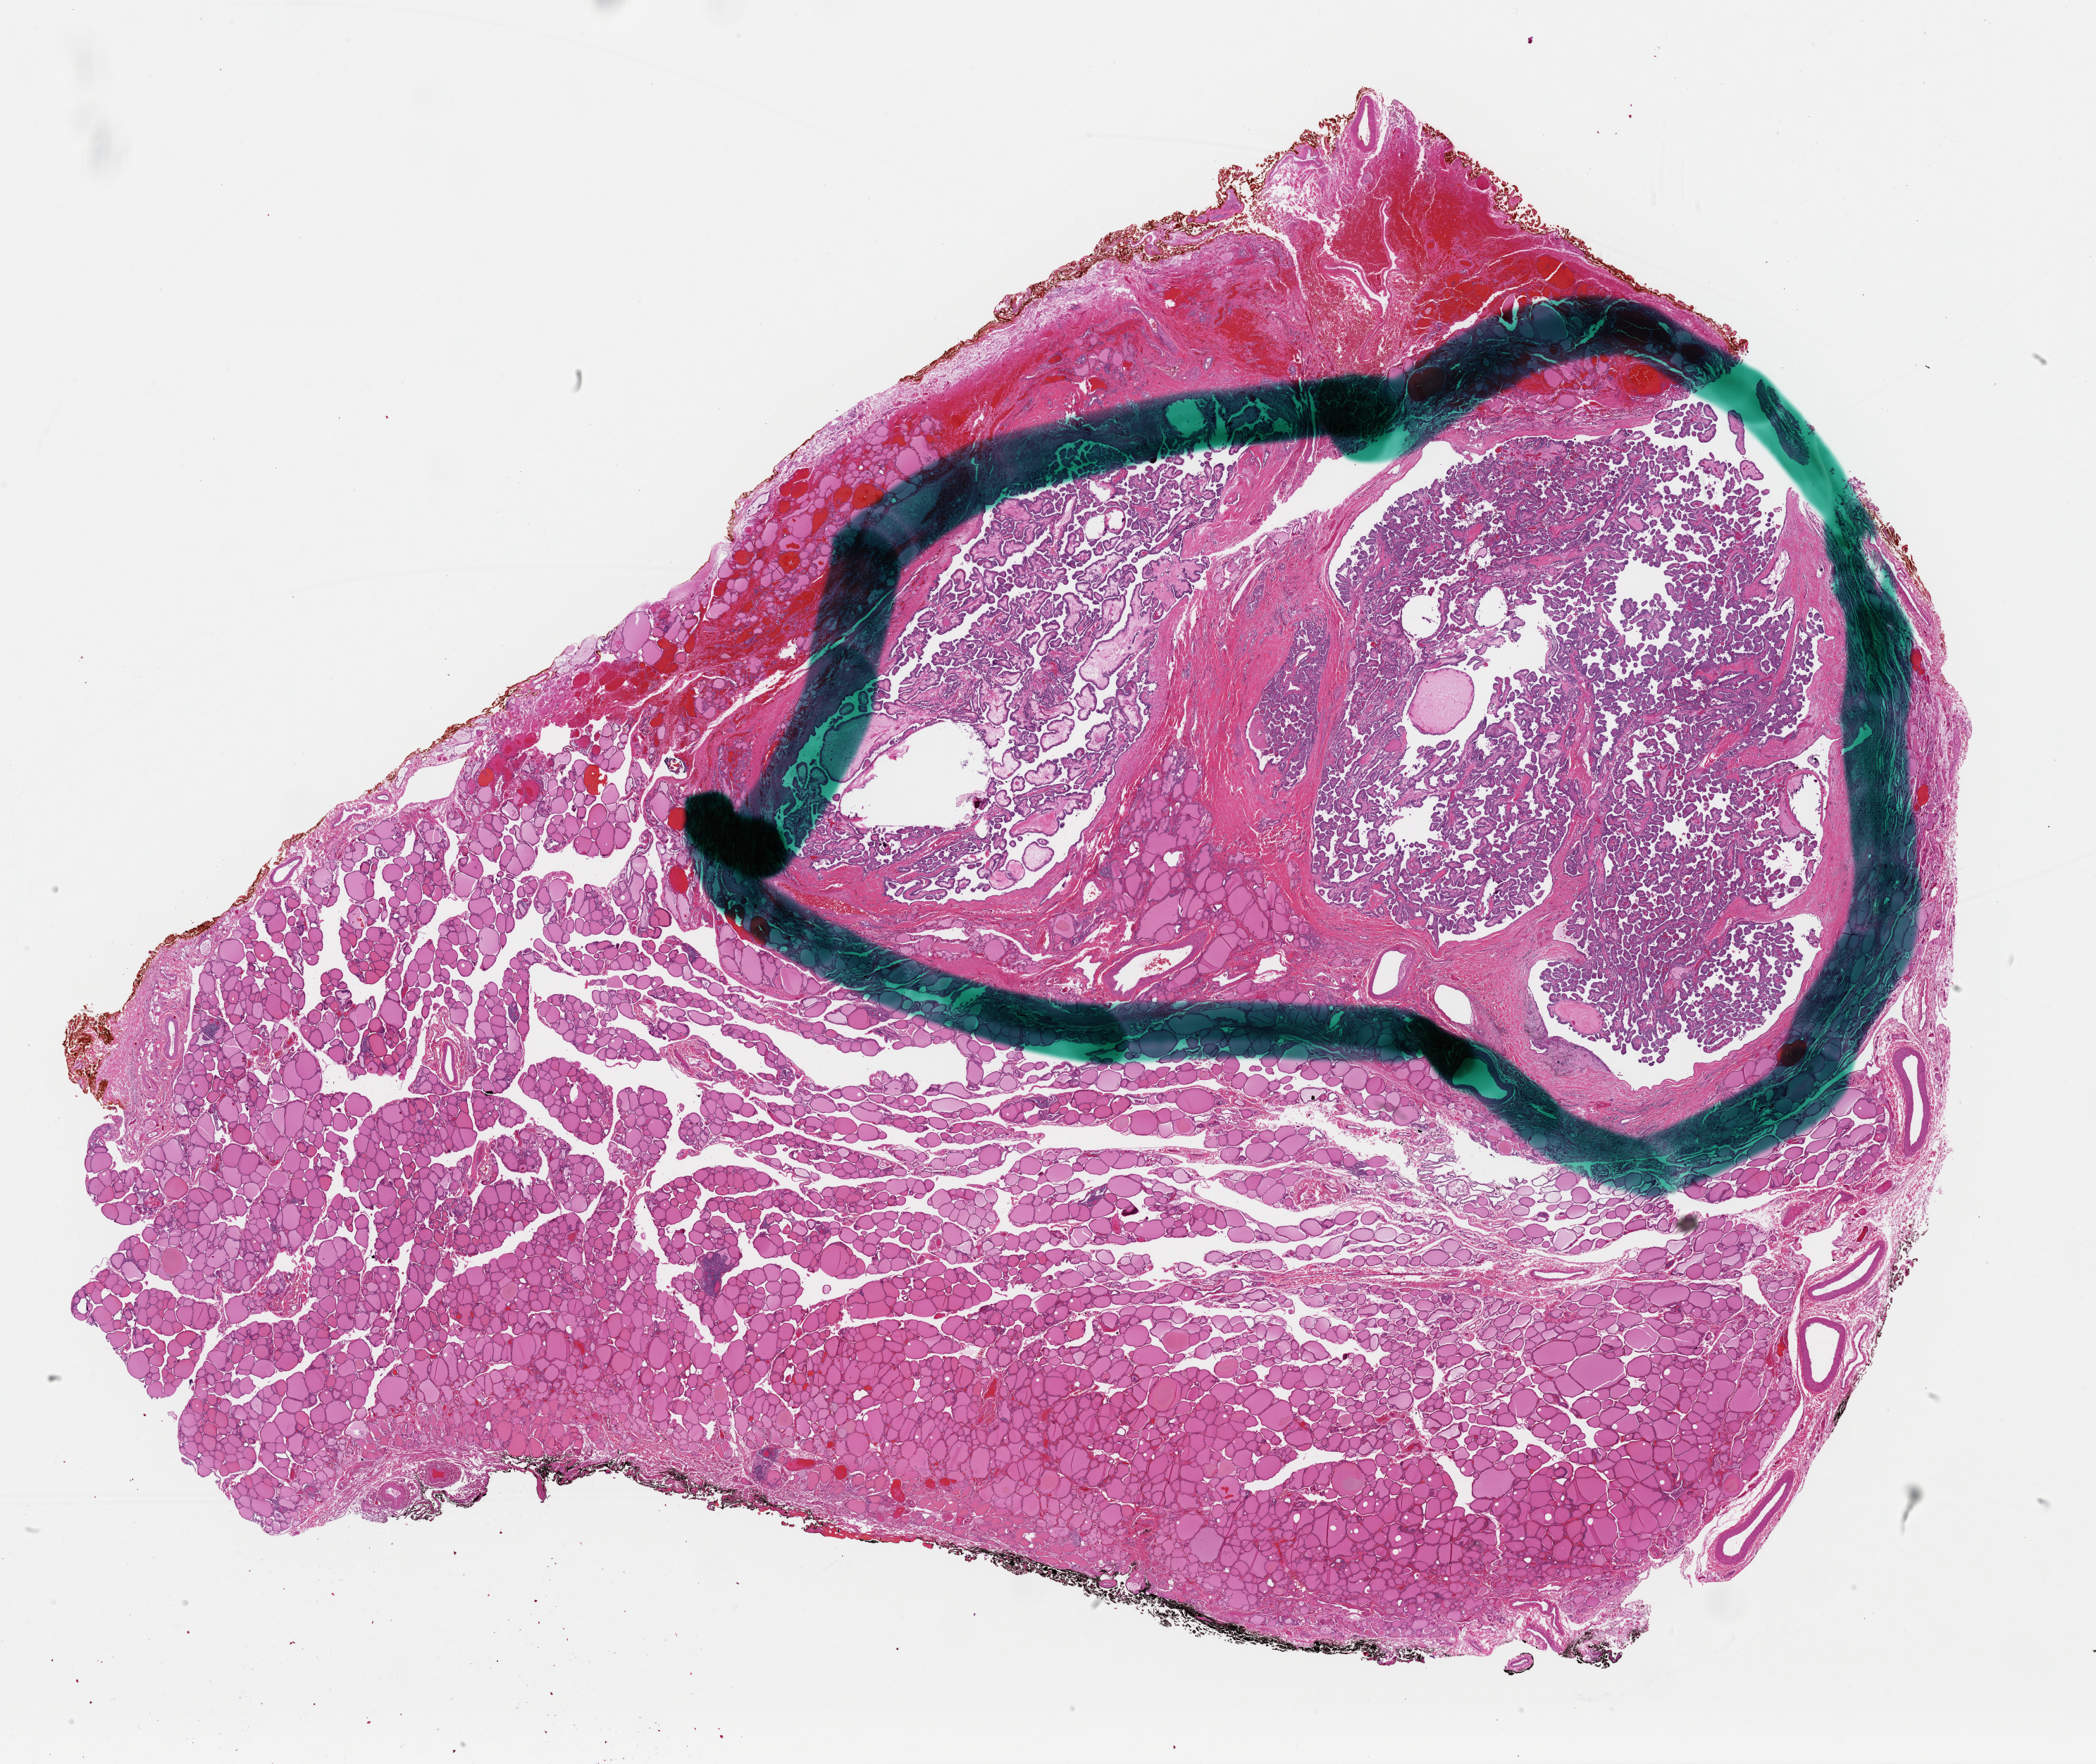
Digitized Hematoxylin and eosin (H&E) stained tissue section (whole slide) — shown as a low-resolution overview of the whole scanned area (about 23.5 x 19.8 mm, from a 40x scan). Formalin-fixed paraffin-embedded (FFPE) diagnostic section. Thyroid, primary tumour sample. Female, age 28 years at initial diagnosis.
* diagnosis: Papillary adenocarcinoma, NOS (thyroid gland)
* AJCC pathologic stage: I
* TNM: T3 N1a MX
* lymph nodes positive (case pathology): 2 of 14 examined